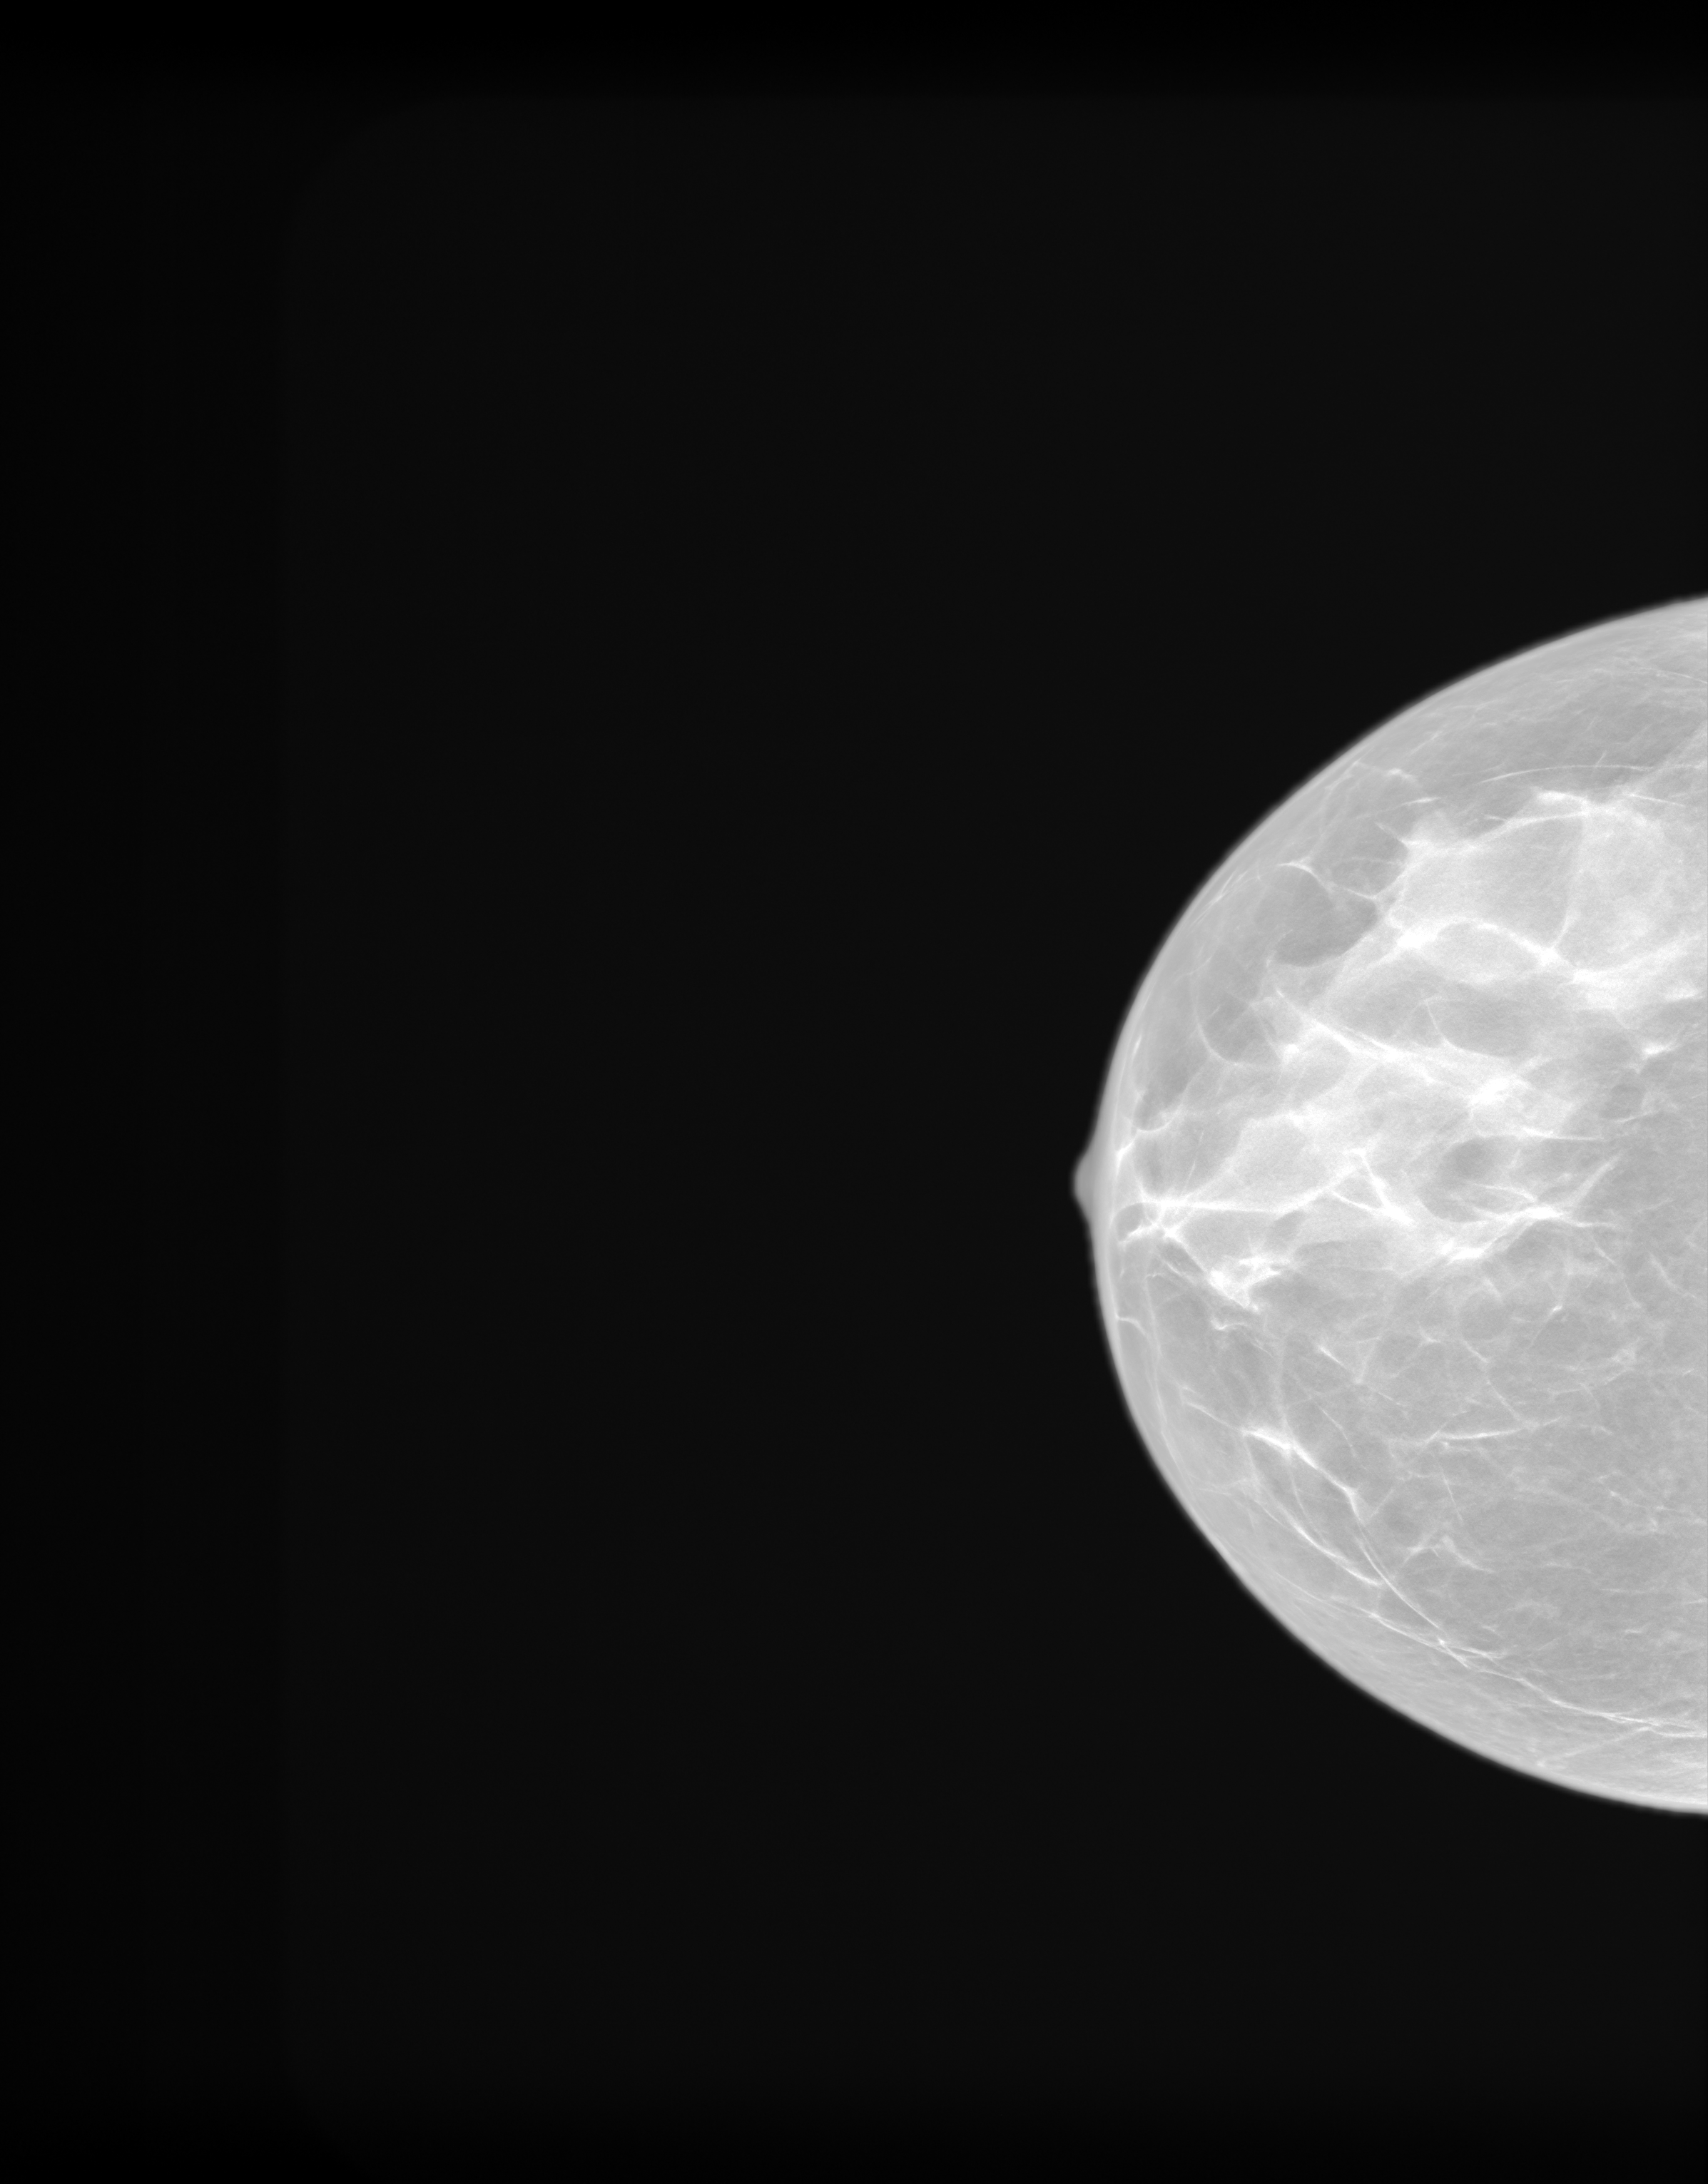
Synthetic 2-D view generated from a tomosynthesis acquisition (not an FFDM exposure), right breast, cranio-caudal projection, screening examination. Patient aged 51 years (female).
Breast density at the screening exam (both breasts): heterogeneously dense (BI-RADS density category c). Final BI-RADS category for the screening round (tomosynthesis exam, both breasts): category 1. Recall: no recall after this screen.